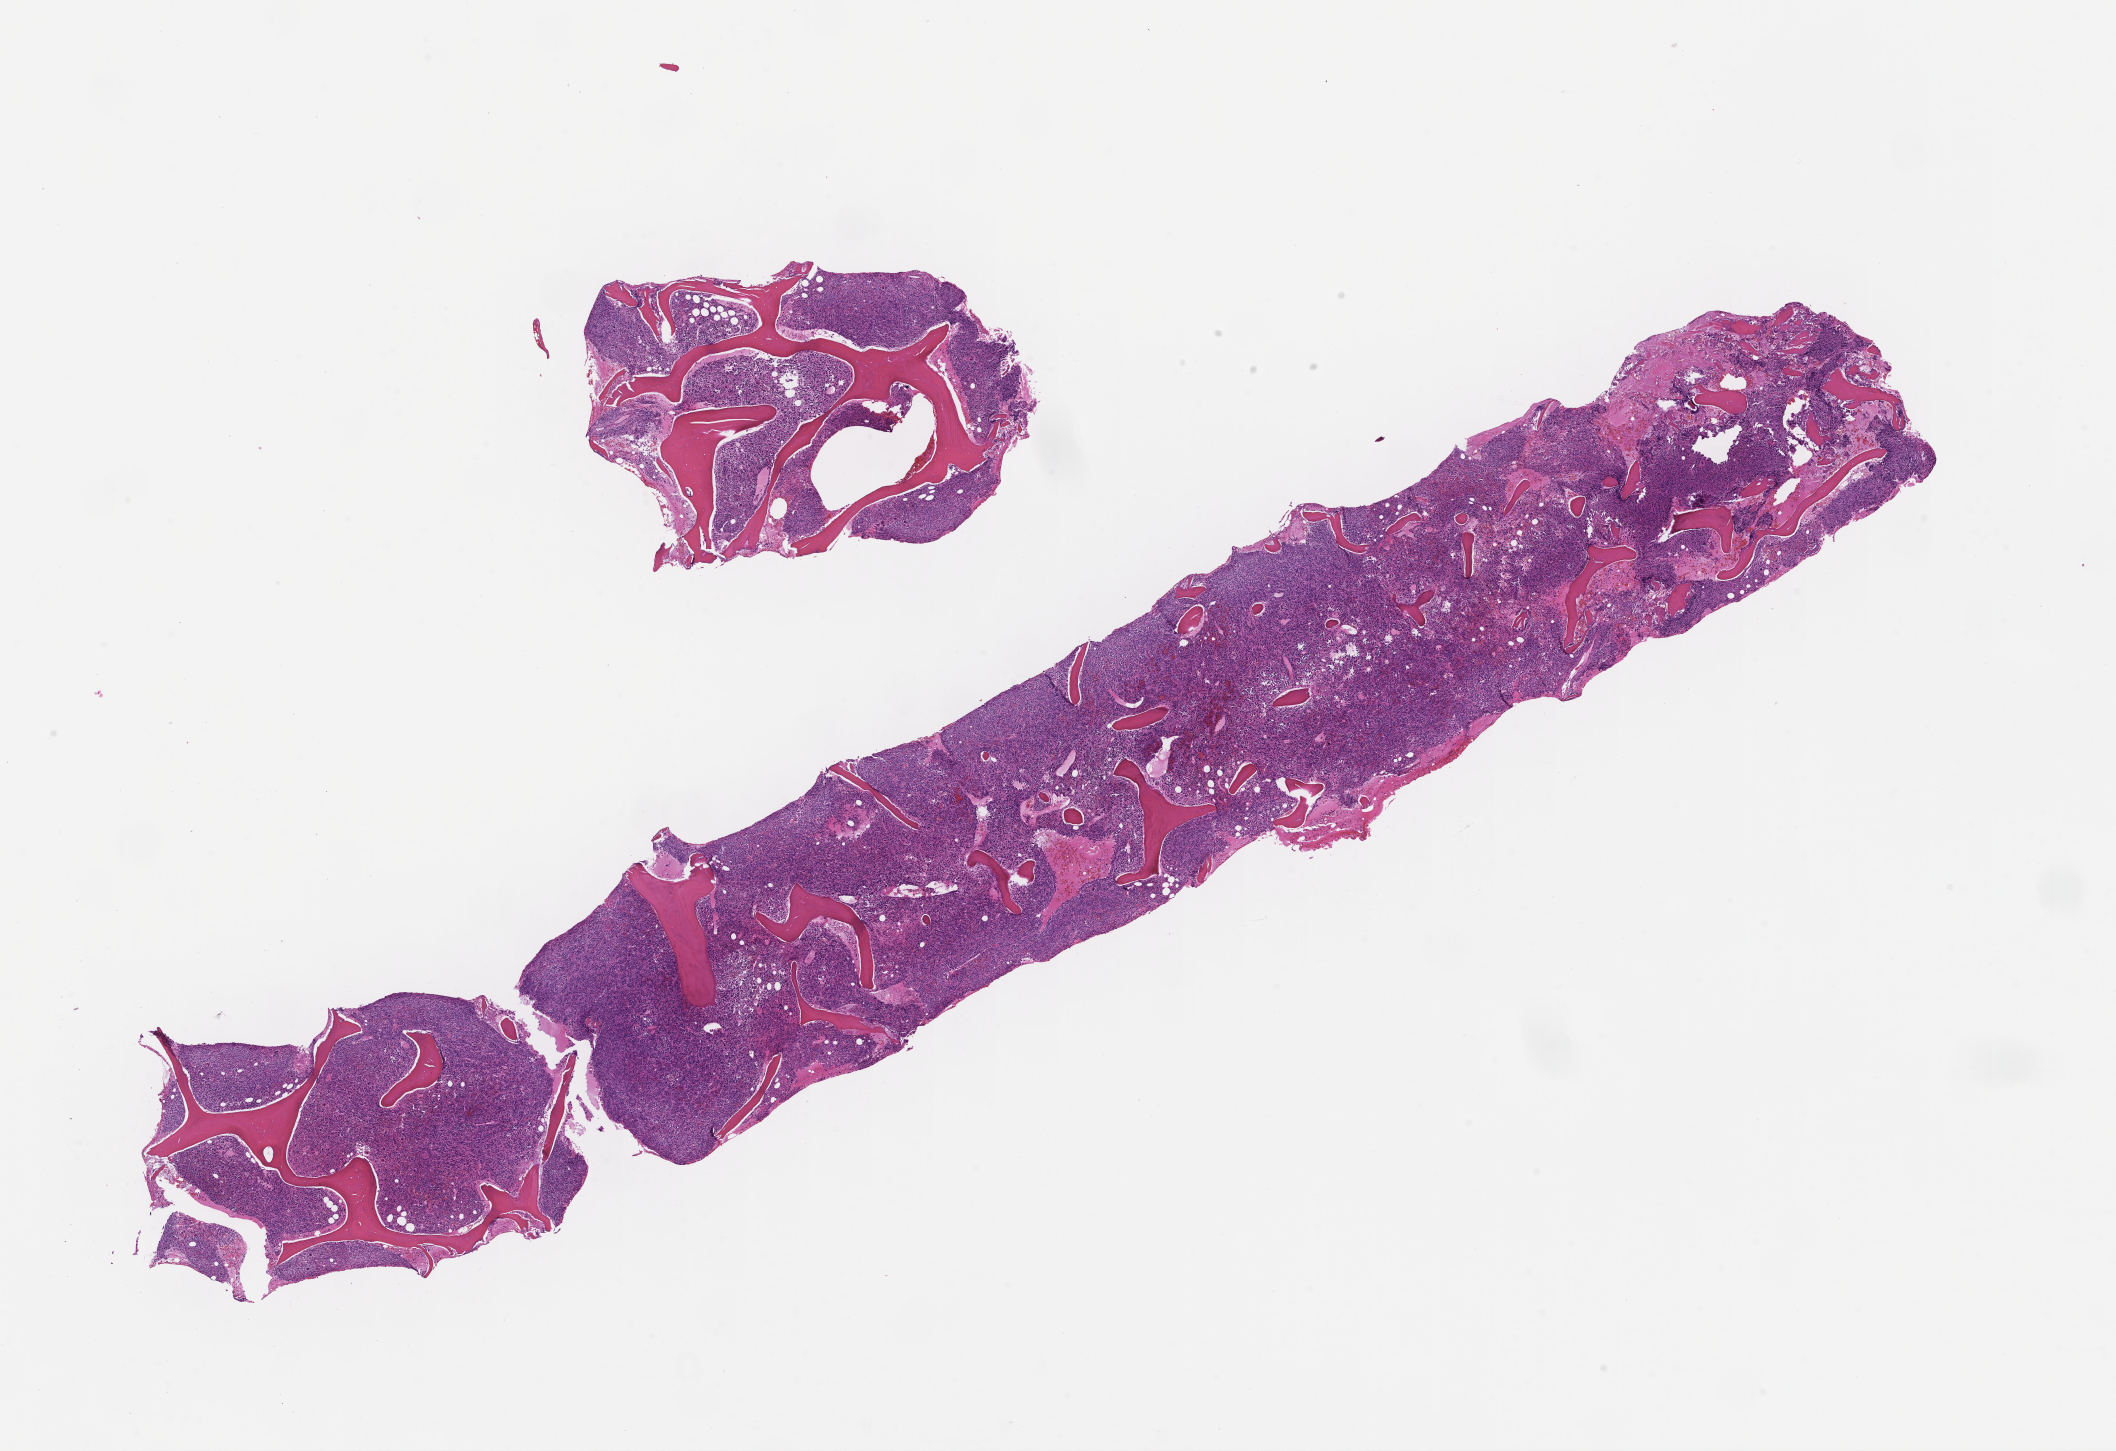
Whole-slide image, hematoxylin and eosin (H&E) stain, shown as a low-resolution overview of the whole scanned area (about 17.1 x 11.7 mm). Formalin-fixed paraffin-embedded section. Tissue site: bone marrow. Specimen time point: archival tissue. Patient: male.
This section: primary tumour tissue. Diagnosis: Plasma Cell Myeloma.